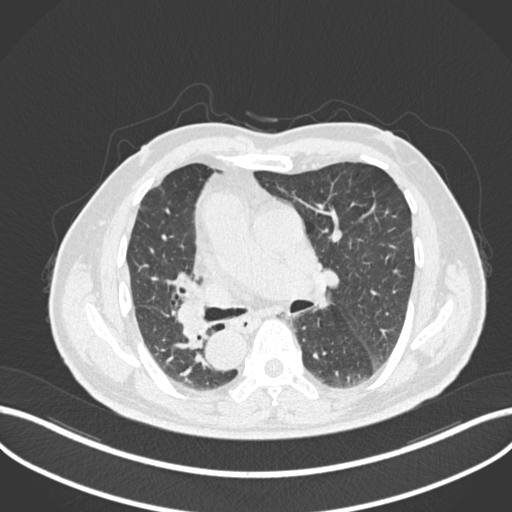
Chest CT, one axial slice. Slice 123 of 206 in the series (ordered by position). 120 kVp. Lung window (W 1500 / L -600 HU). 1 mm slice thickness. 512 × 512 image matrix, field of view 400 × 400 mm. Male patient, age 67 years. From the clinical record (not read from this slice): clinical TNM (as recorded): T2a N0 M0.
Annotated regions visible in this slice (bounding box drawn by a radiologist):
- lung tumour (recorded histology: squamous cell carcinoma): box from (x=173, y=293) to (x=212, y=350) px